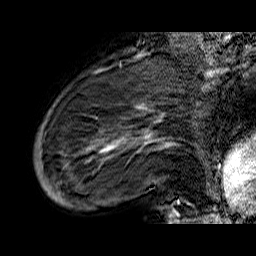
Breast MRI (dynamic contrast-enhanced), one sagittal slice. Slice 13 of 60 in the series (ordered by position). Dynamic contrast-enhanced series, time point 2 of 6 at this slice position (early post-contrast). 1.5 T. TE 6.5 ms, TR 32.9 ms. 4 mm slice thickness. 256 × 256 image matrix, field of view 200 × 200 mm. Female patient. Case-level facts recorded for this patient, not image findings: setting: breast cancer imaged before/during neoadjuvant chemotherapy; receptor status: HR-positive, HER2-negative.
Structures marked on this image (semi-automatic segmentation, software-assisted and operator-edited):
- analysis volume of interest (the breast-tissue region the enhancement analysis was run in; not a lesion): bounding box (x1, y1, x2, y2) in pixels: (34, 74, 176, 210)
- tumour enhancement mask (voxels above the 100 % enhancement threshold inside the analysis volume of interest): (39, 106, 165, 195)